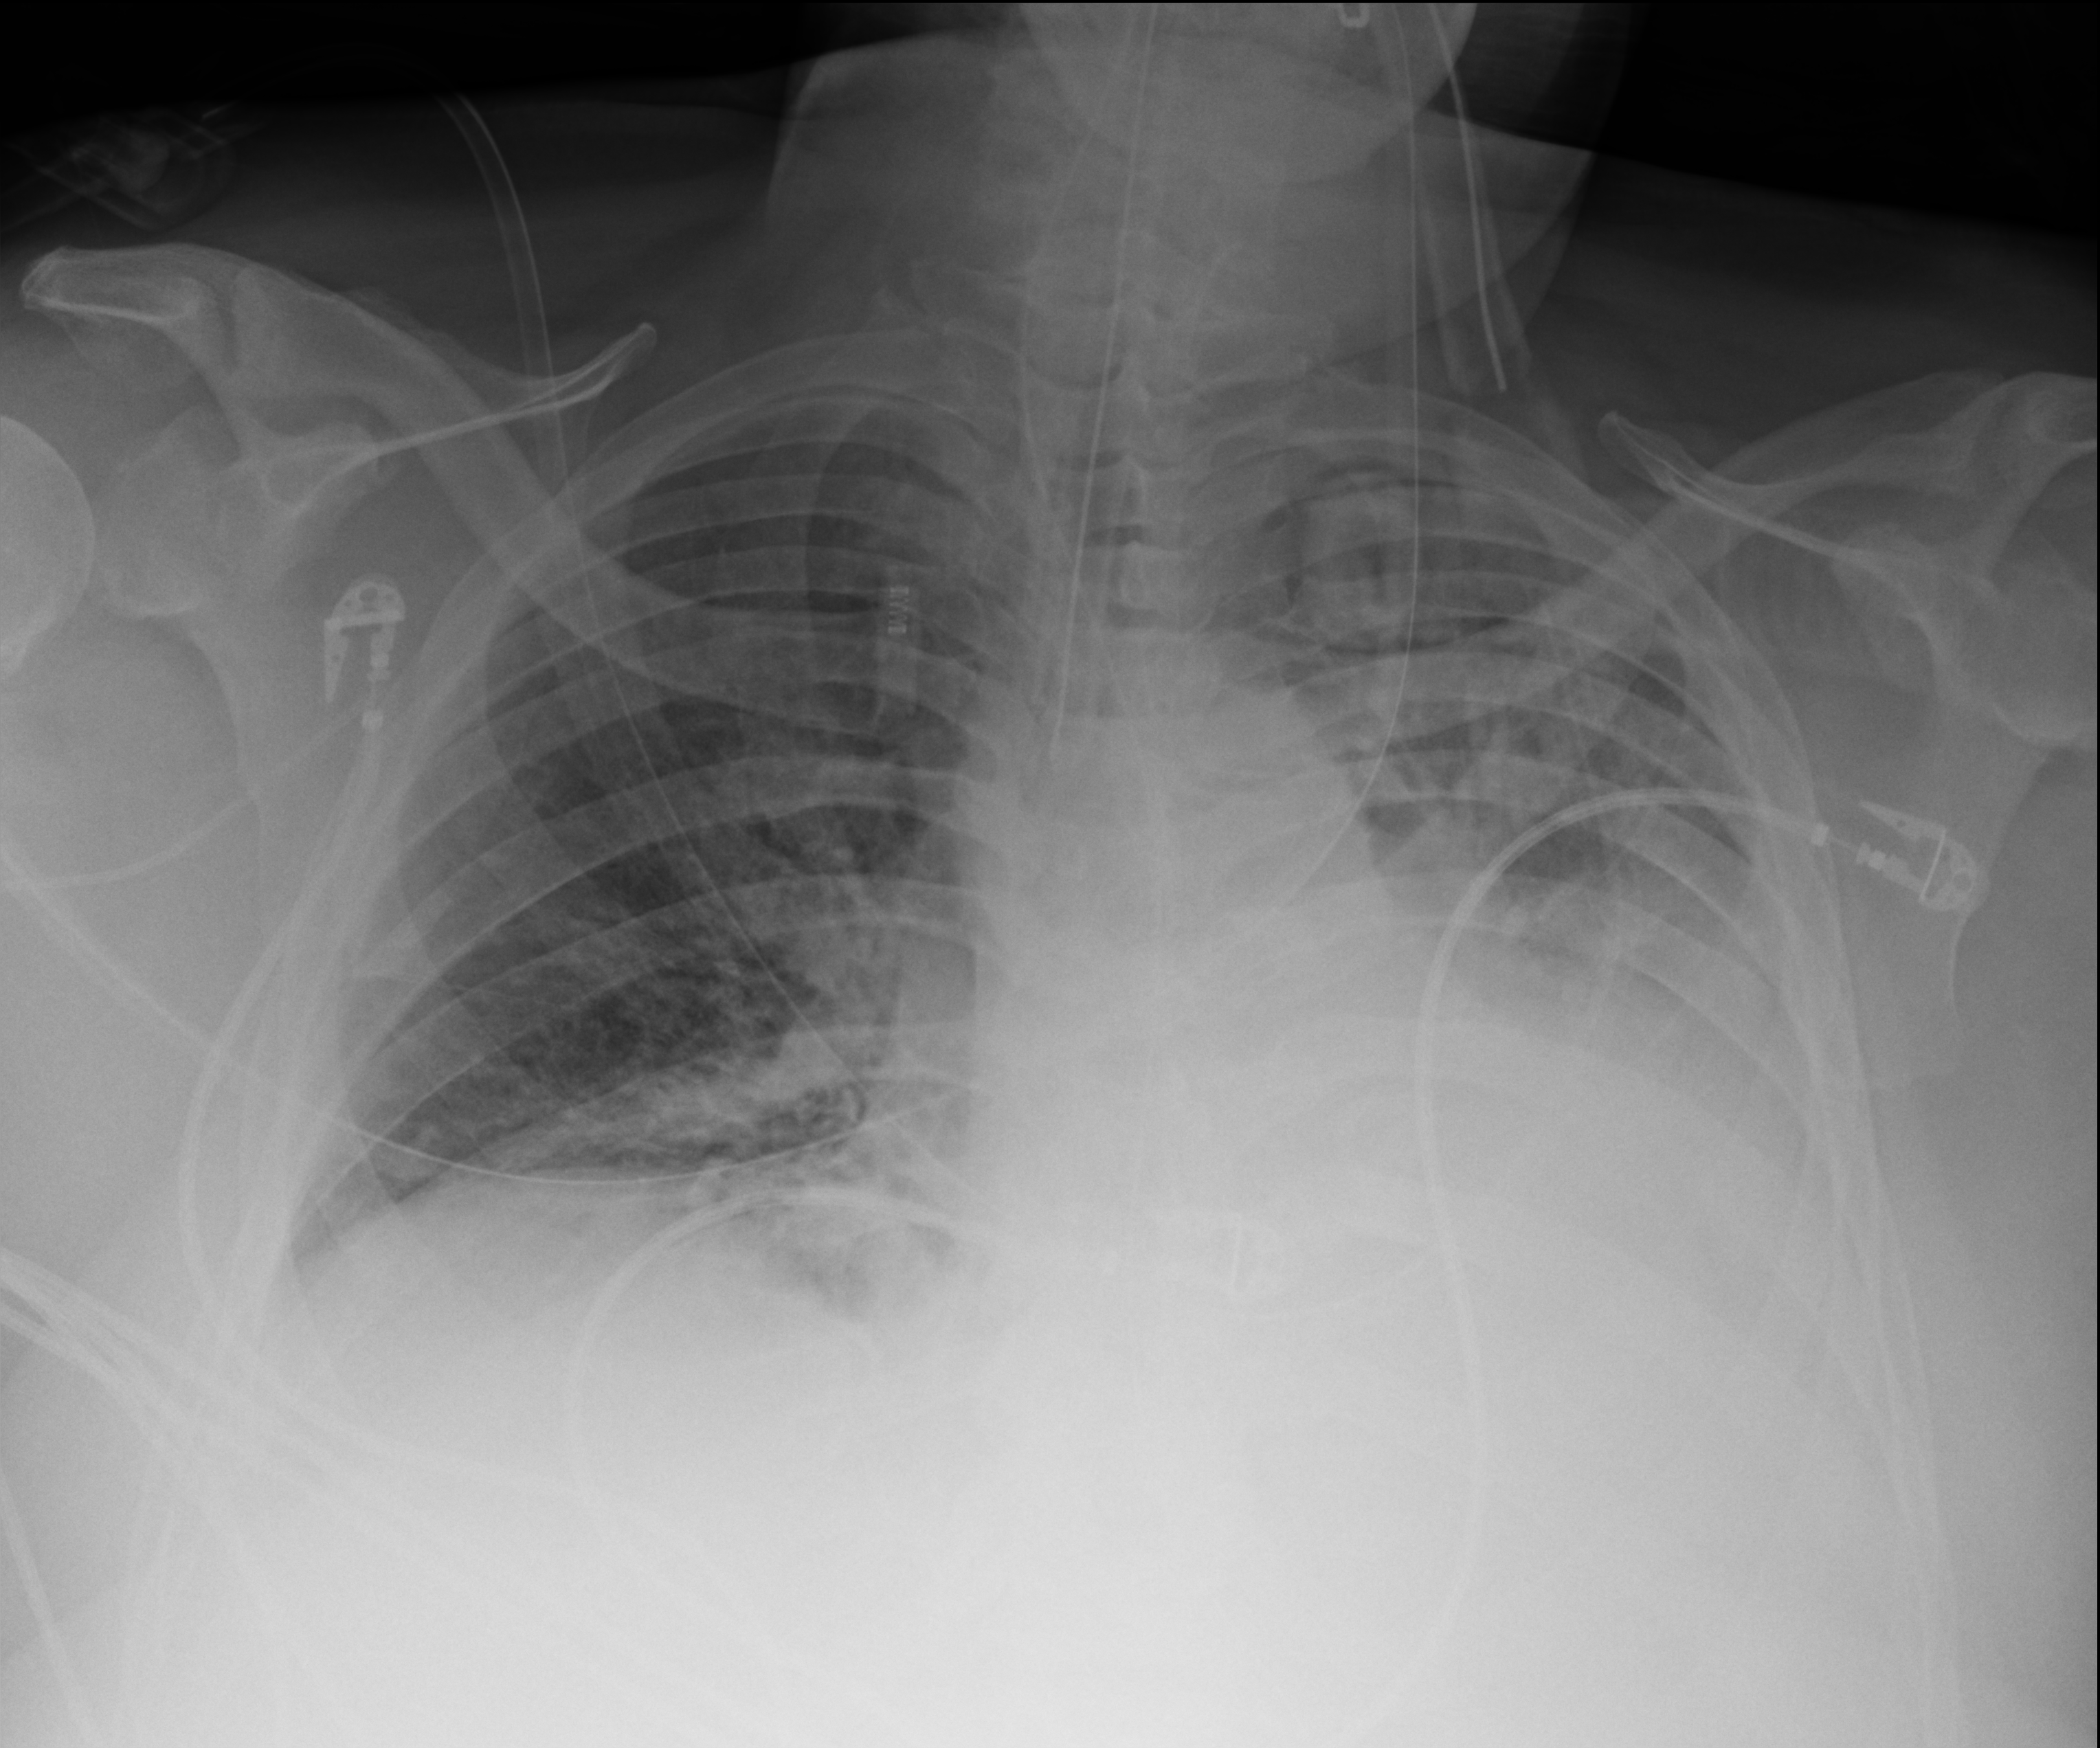
Chest X-ray (portable), anteroposterior (AP) projection. Patient hospitalised with COVID-19; male, aged 60–74 years.
Hospital-stay facts (about this admission, not read from this image; timing relative to this image not recorded):
- hypertension (admission record): yes